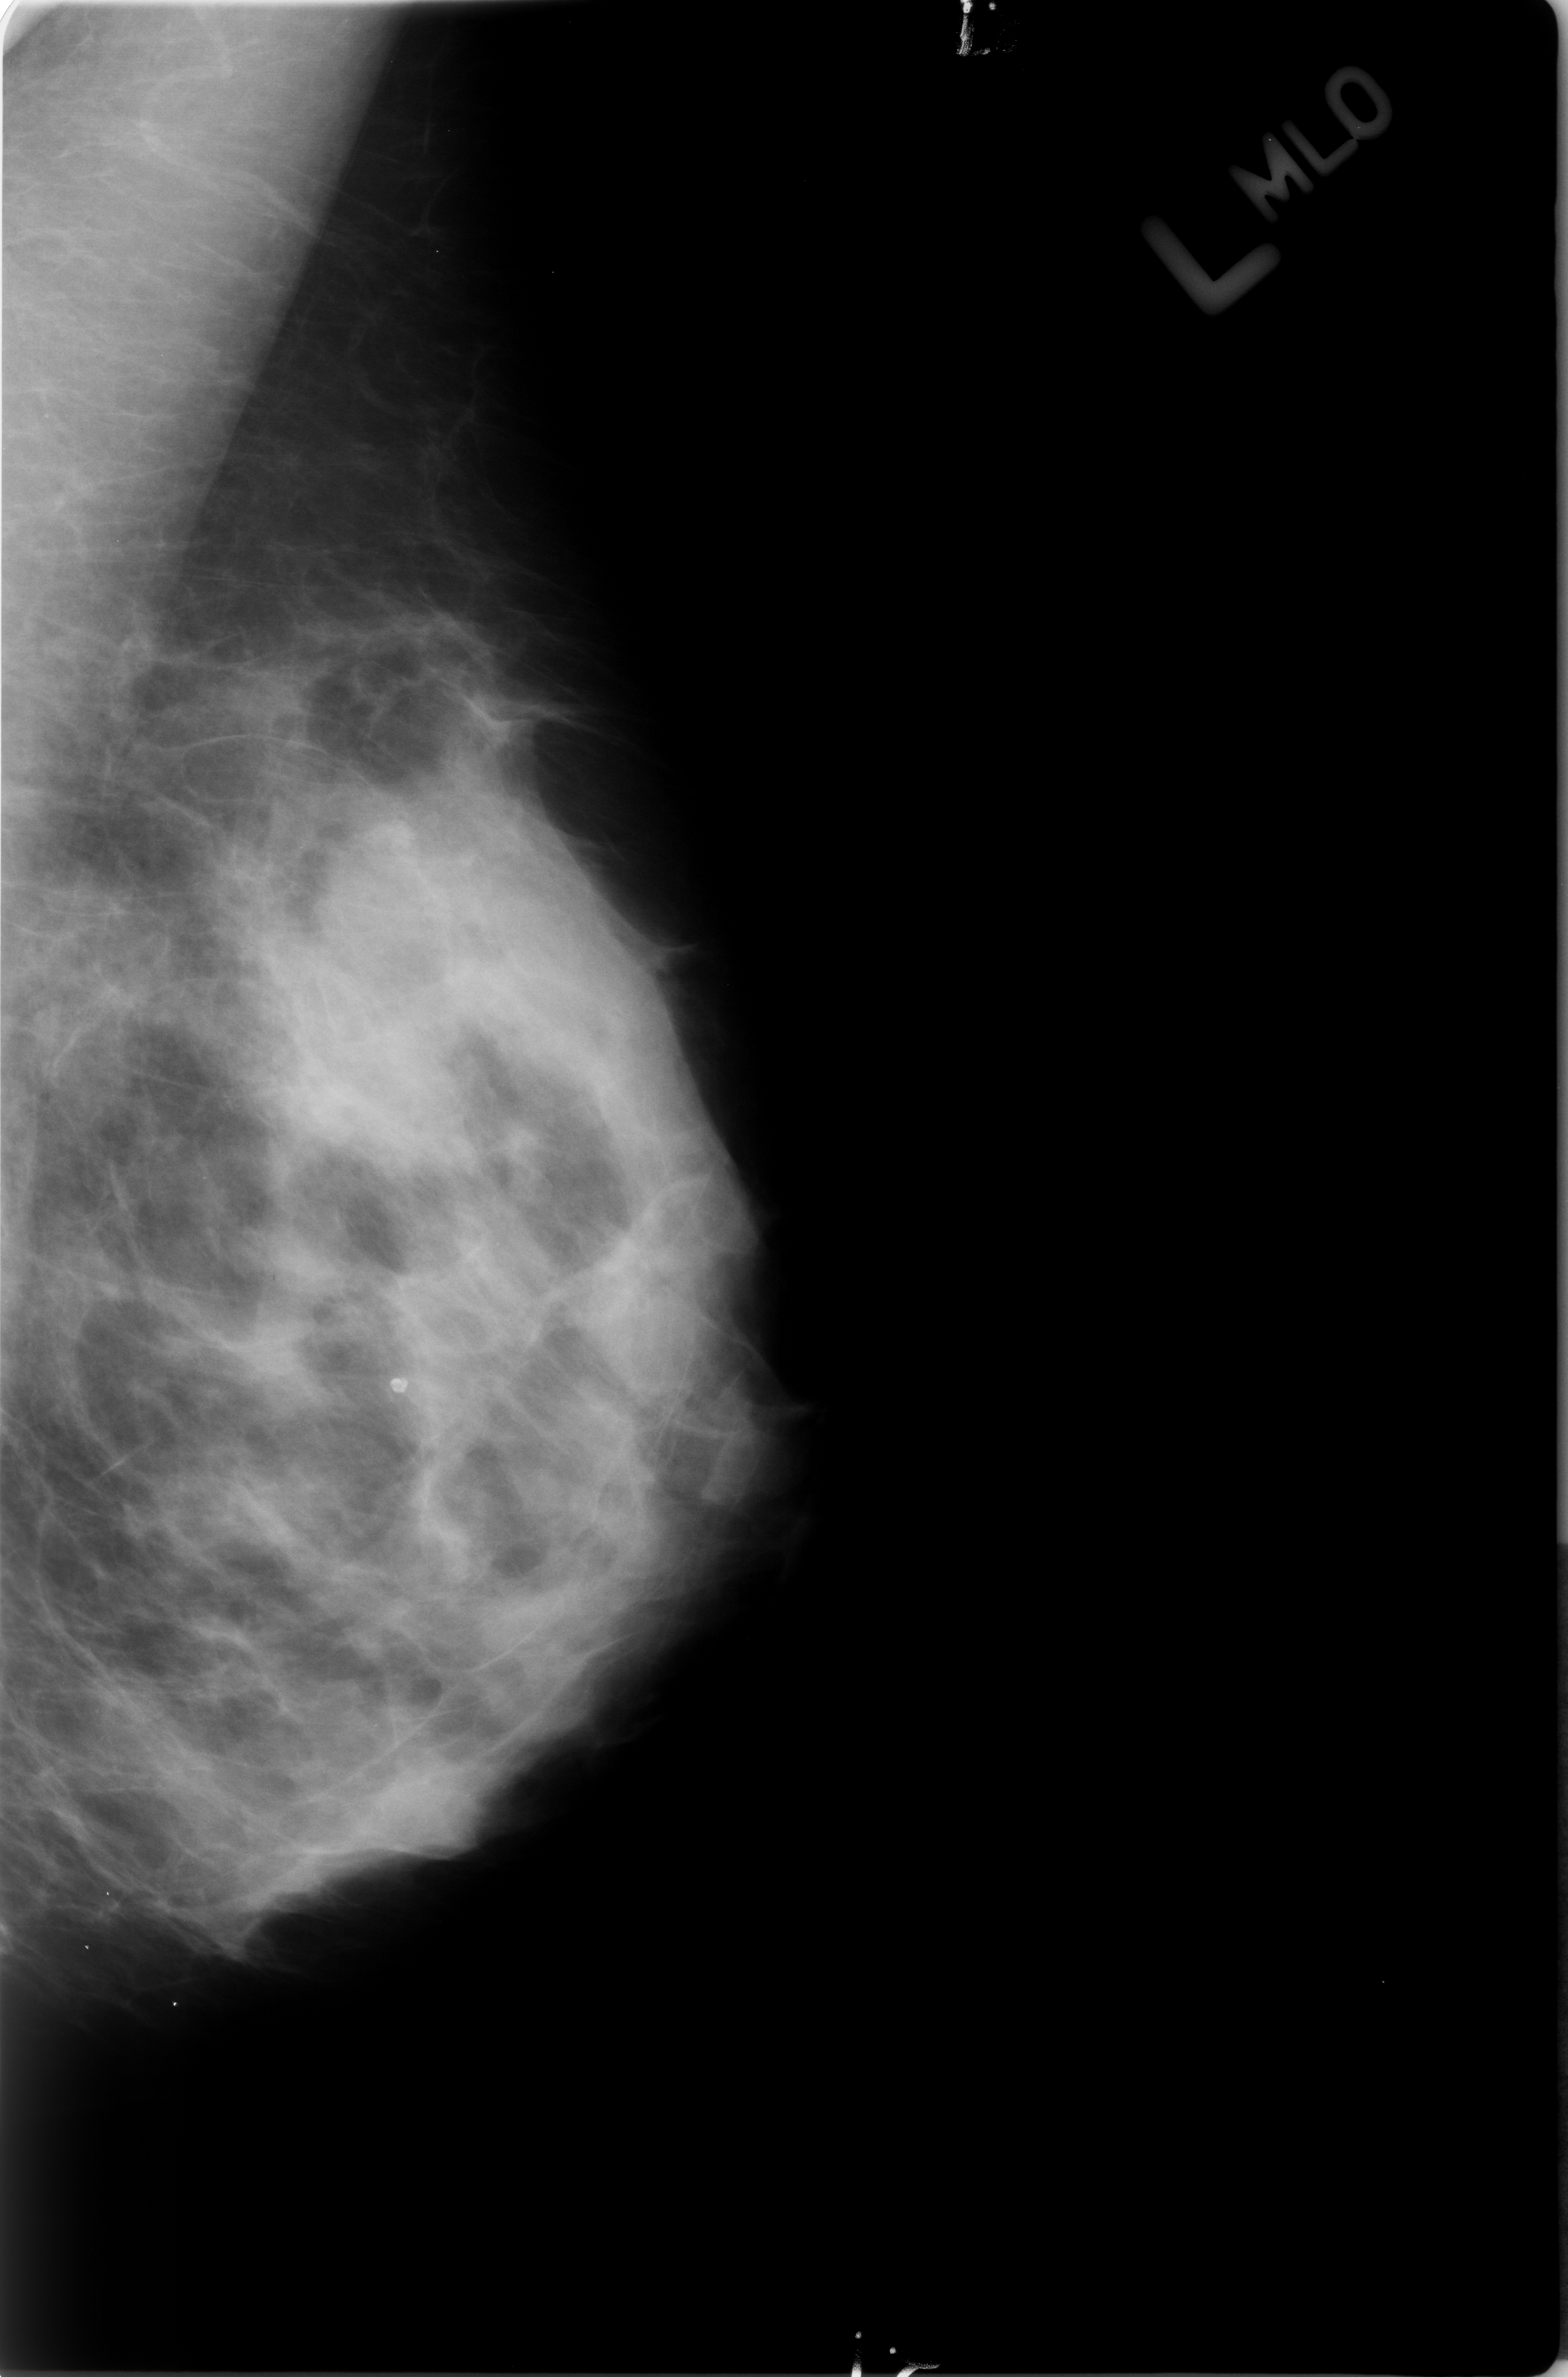
Scanned film-screen mammogram; left breast; MLO view; 1568 × 2377 image matrix.
Expert-marked regions of interest on this film, with their recorded descriptors:
- calcifications, morphology lucent center; BI-RADS assessment category 2; outcome (as recorded, no biopsy): benign without callback (not worked up further): bounding box (x1, y1, x2, y2) in pixels: (389, 1368, 412, 1395)